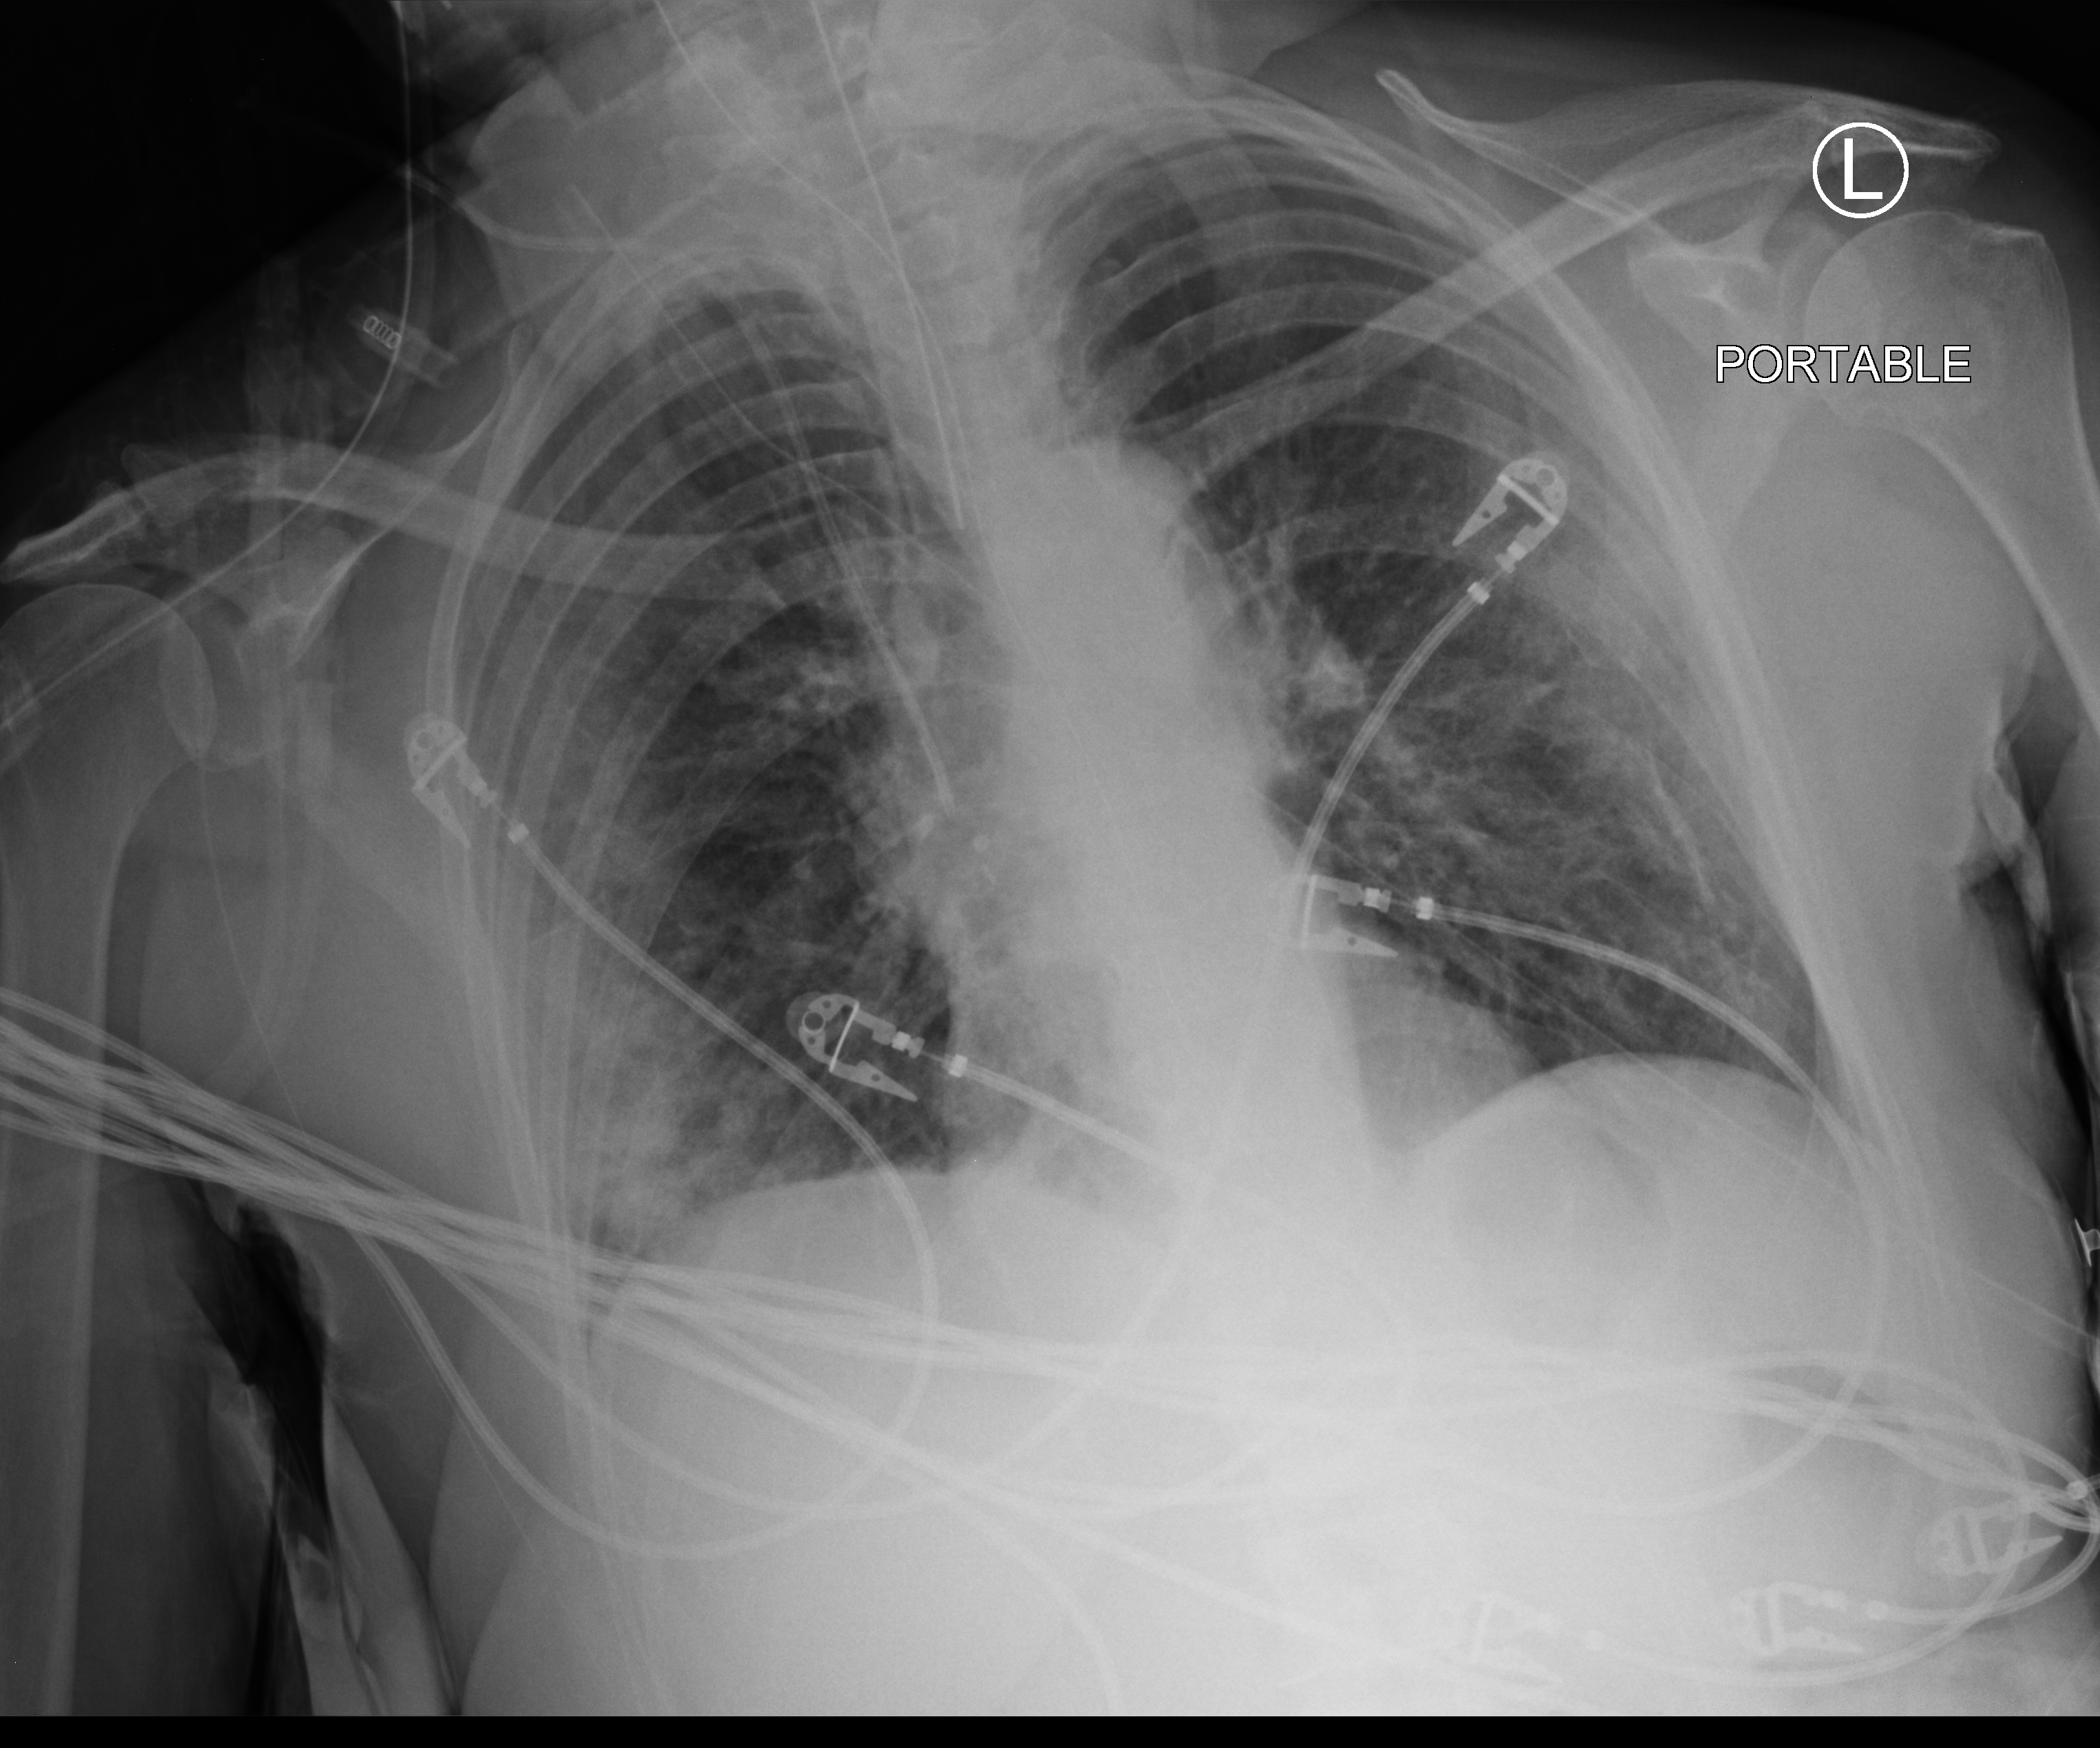
Bedside chest radiograph (computed radiography), anteroposterior (AP) projection. Patient hospitalised with COVID-19; female, aged 60–74 years.
Hospital-stay facts (about this admission, not read from this image; timing relative to this image not recorded): admitted to intensive care during this hospital stay: yes; other chronic lung disease (admission record): no.